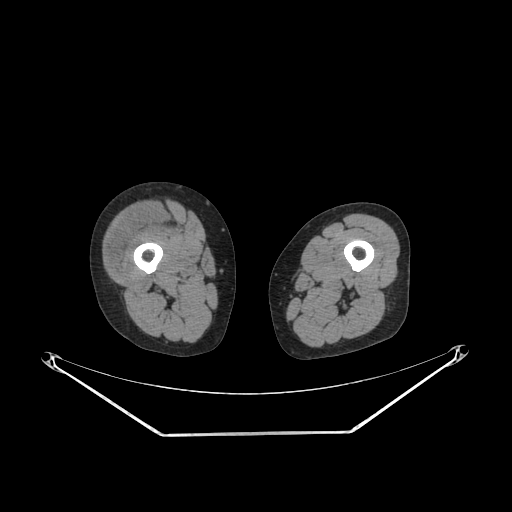
CT of an extremity soft-tissue mass (from a PET/CT study), one axial slice. Slice 220 of 311 in the series (ordered by position). Reconstruction kernel SOFT. 140 kVp. Soft-tissue window (W 400 / L 40 HU). 3.75 mm slice thickness. 512 × 512 image matrix. Female patient. From the clinical record (not read from this slice): histological type: pleiomorphic undifferentiated sarcoma; grade: high; site of the primary tumour: right quadricep.
Outlined on this slice (expert contour drawn on MRI and transferred to this co-registered scan by the dataset authors):
- tumour plus oedema (research contour): bounding box [x1, y1, x2, y2] px = [107, 206, 161, 268]